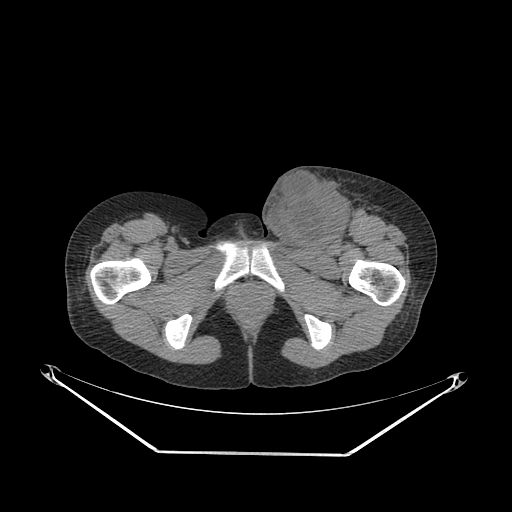
CT of an extremity soft-tissue mass (from a PET/CT study), one axial slice; slice 59 of 267 in the series (ordered by position); reconstruction kernel SOFT; soft-tissue window (W 400 / L 40 HU); 512 × 512 image matrix, field of view 500 × 500 mm. Female patient. From the clinical record (not read from this slice): histological type: leiomyosarcoma; grade: high; site of the primary tumour: groin.
Structures marked on this image (expert contour drawn on MRI and transferred to this co-registered scan by the dataset authors):
- gross tumour volume including surrounding oedema: bounding box (x1, y1, x2, y2) in pixels: (258, 167, 371, 252)
- gross tumour volume (mass): (263, 173, 350, 250)